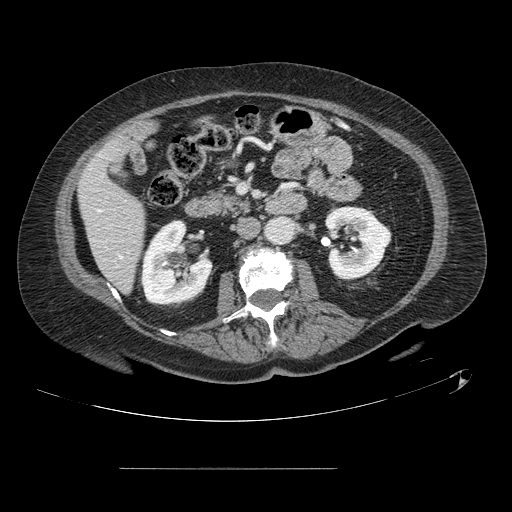
Contrast-enhanced abdominal CT, one axial slice. Slice 39 of 148 in the series (ordered by position). 120 kVp. Soft-tissue window (W 400 / L 40 HU). 512 × 512 image matrix, field of view 439 × 439 mm. Female patient, age 75 years. From the clinical record (not read from this slice): diagnosis: colorectal cancer liver metastases, imaged before liver resection; multiple liver metastases: no; largest metastasis: 2.4 cm.
Structures marked on this image (expert manual segmentation):
- hepatic veins: bounding box [x1, y1, x2, y2] px = [98, 210, 122, 258]
- liver: [80, 140, 145, 292]
- planned liver remnant (the part of the liver to remain after resection): [80, 139, 145, 292]